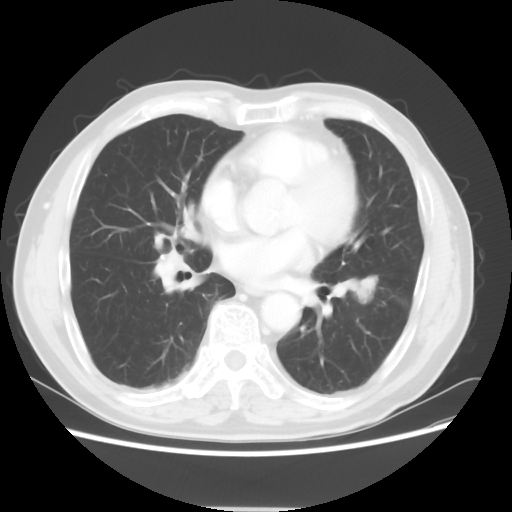
Chest CT, one axial slice; position 26 of 64 along the scan axis; lung window (W 1500 / L -600 HU); 5 mm slice thickness; 512 × 512 image matrix, field of view 366 × 366 mm. Patient: male, 71 years. From the clinical record (not read from this slice): clinical TNM (as recorded): T1c N1 M0; histopathological grade: G2-3.
Annotated regions visible in this slice (rectangle marked by the reading radiologist):
- lung tumour (recorded histology: adenocarcinoma): box from (x=343, y=267) to (x=386, y=307) px